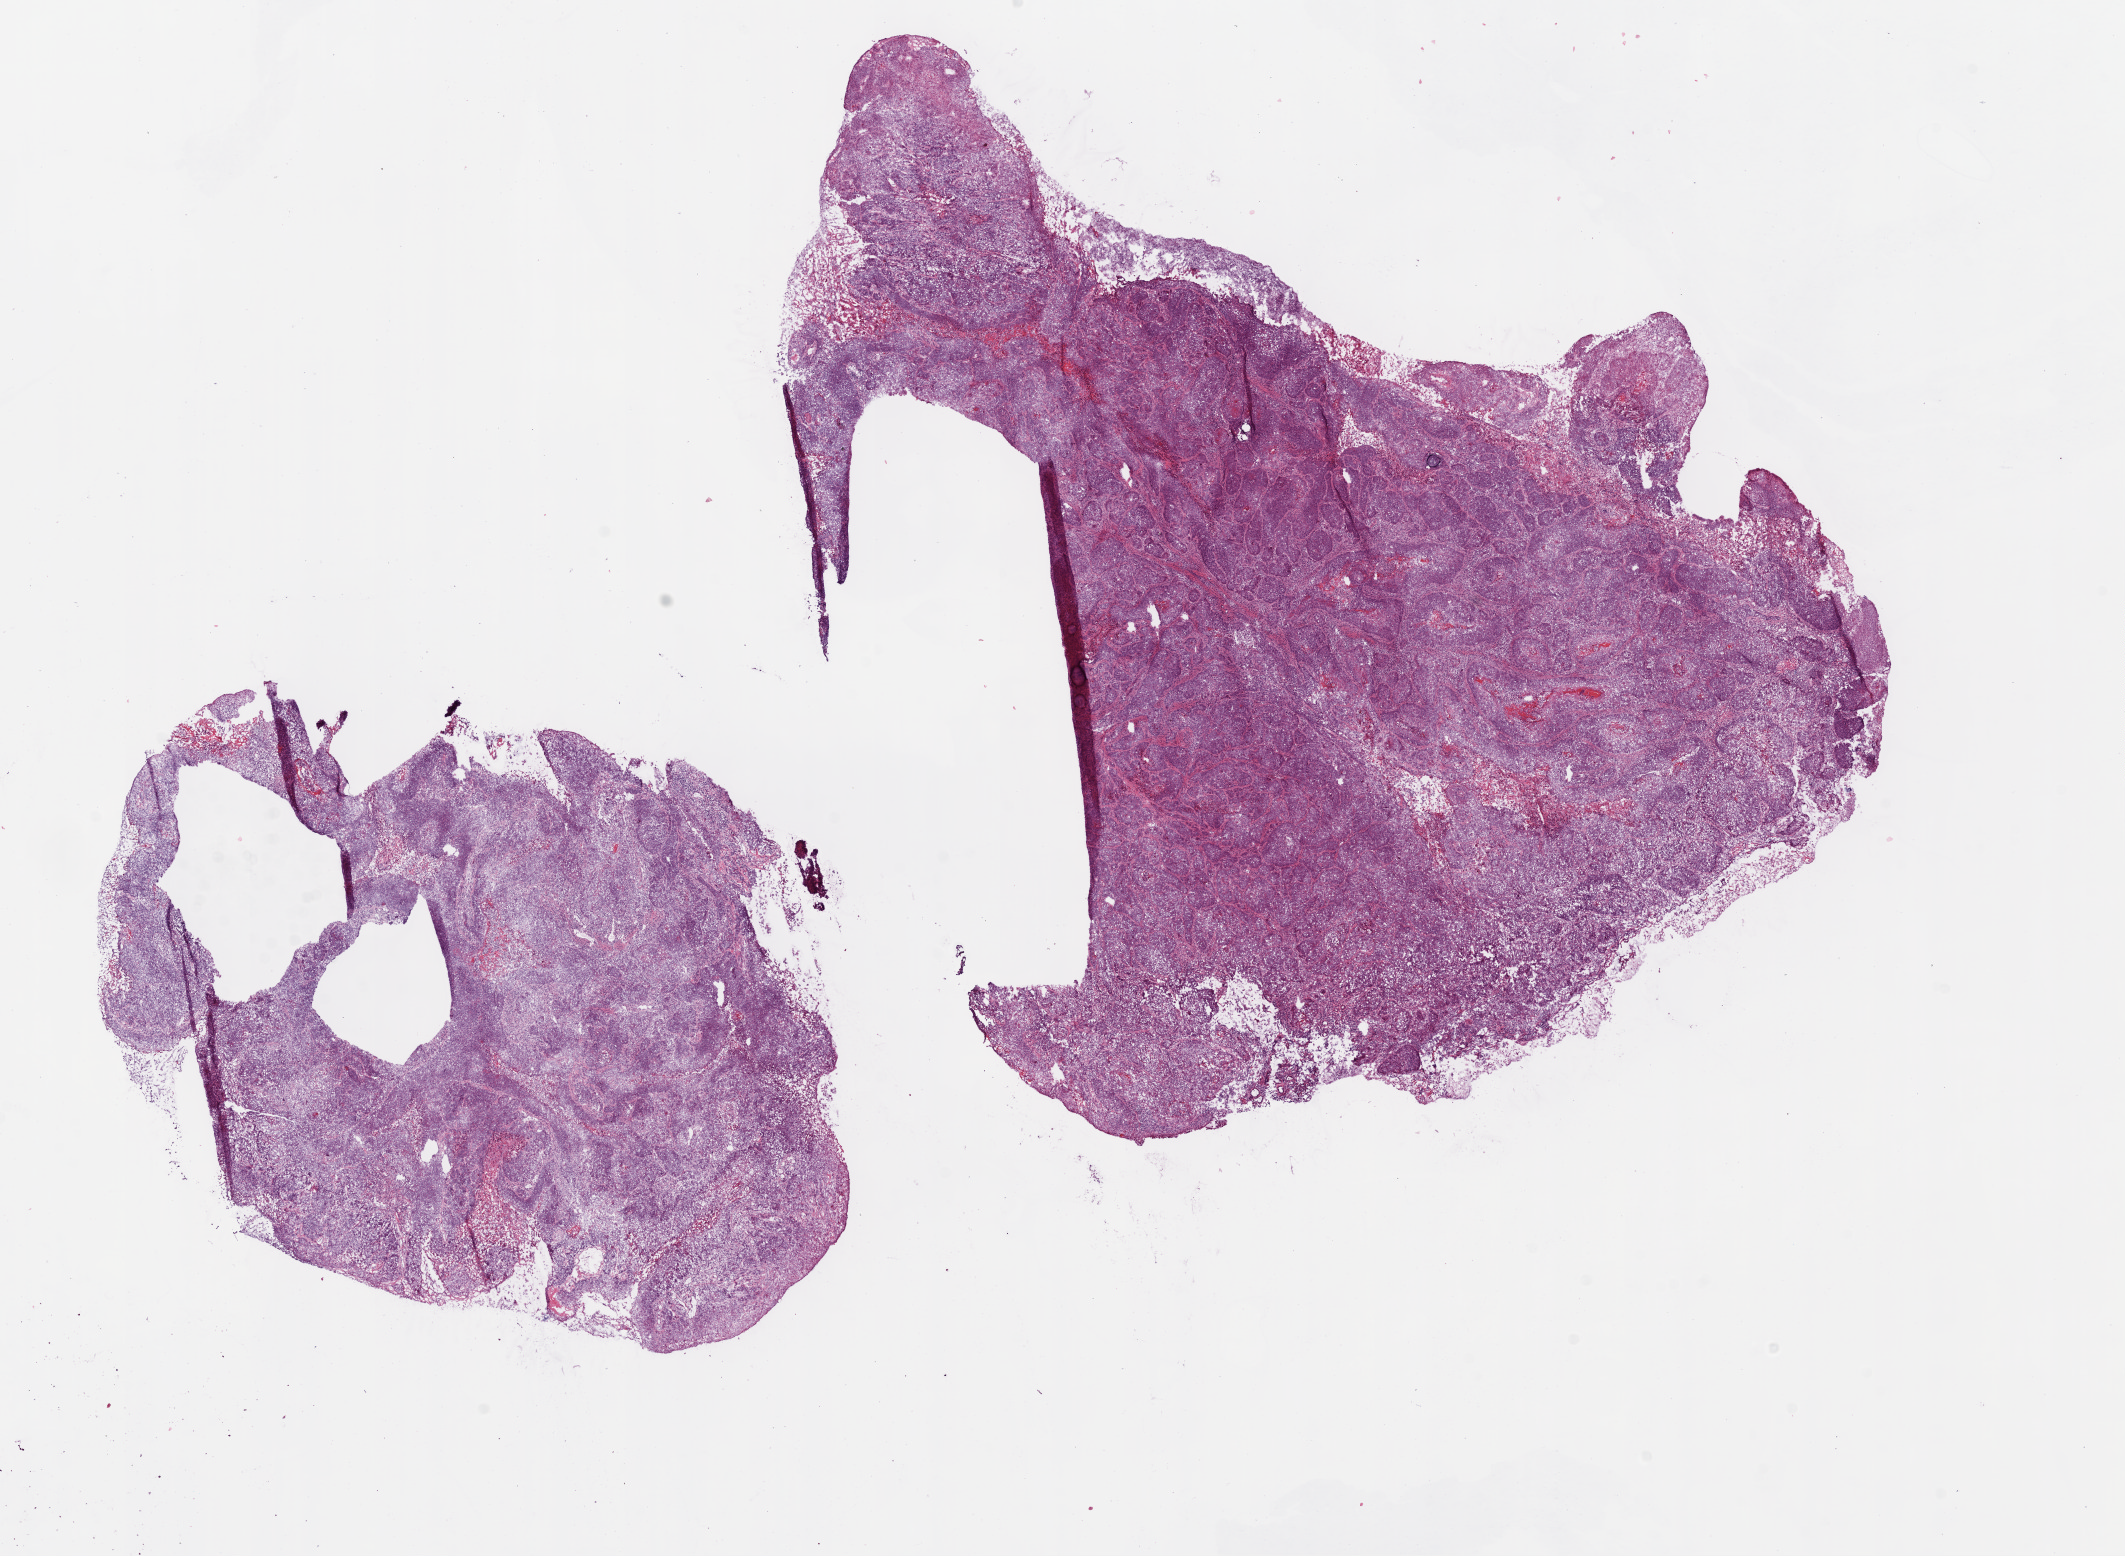
Whole-slide histology image, H&E-stained — low-resolution overview of the scanned area, about 17.1 x 12.5 mm (slide scanned at 20x); frozen section; primary tumour sample from the lung. Male patient; age at initial diagnosis 65 years. Composition of this section per pathologist review: tumour cells 85%, tumour nuclei 90%, normal cells 5%, stromal cells 5%, necrosis 5%.
• AJCC pathologic stage: IB
• pathologic diagnosis: Squamous cell carcinoma, NOS (upper lobe, lung)
• laterality: left